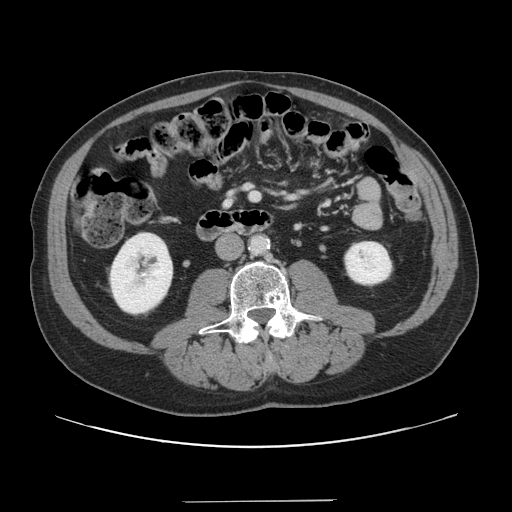
Contrast-enhanced abdominal CT, one axial slice. Slice 32 of 151 in the series (ordered by position). 120 kVp. Intravenous contrast given. Soft-tissue window (W 400 / L 40 HU). 2.5 mm slice thickness. 512 × 512 image matrix. Male patient, age 63 years. Case-level facts recorded for this patient, not image findings: diagnosis: colorectal cancer liver metastases, imaged before liver resection; multiple liver metastases: no; largest metastasis: 2.1 cm; disease in both lobes: no.
Annotated regions visible in this slice (expert manual segmentation):
- portal vein (with intrahepatic branches): bounding box (x1, y1, x2, y2) in pixels: (251, 193, 258, 199)